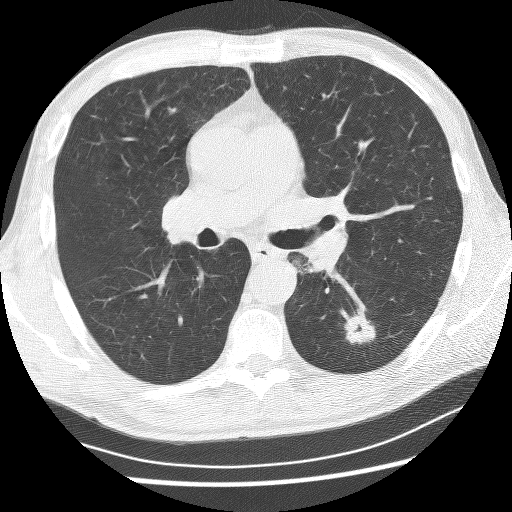
Low-dose screening chest CT, one axial slice. Slice 145 of 253 in the series (ordered by position). Reconstruction kernel BONE. Lung window (W 1500 / L -600 HU). 2.5 mm slice thickness. 512 × 512 image matrix.
Annotated regions visible in this slice (manually delineated by an expert):
- lesion 1 (tumor, lower lobe of left lung): bounding box (x1, y1, x2, y2) in pixels: (340, 309, 376, 344)